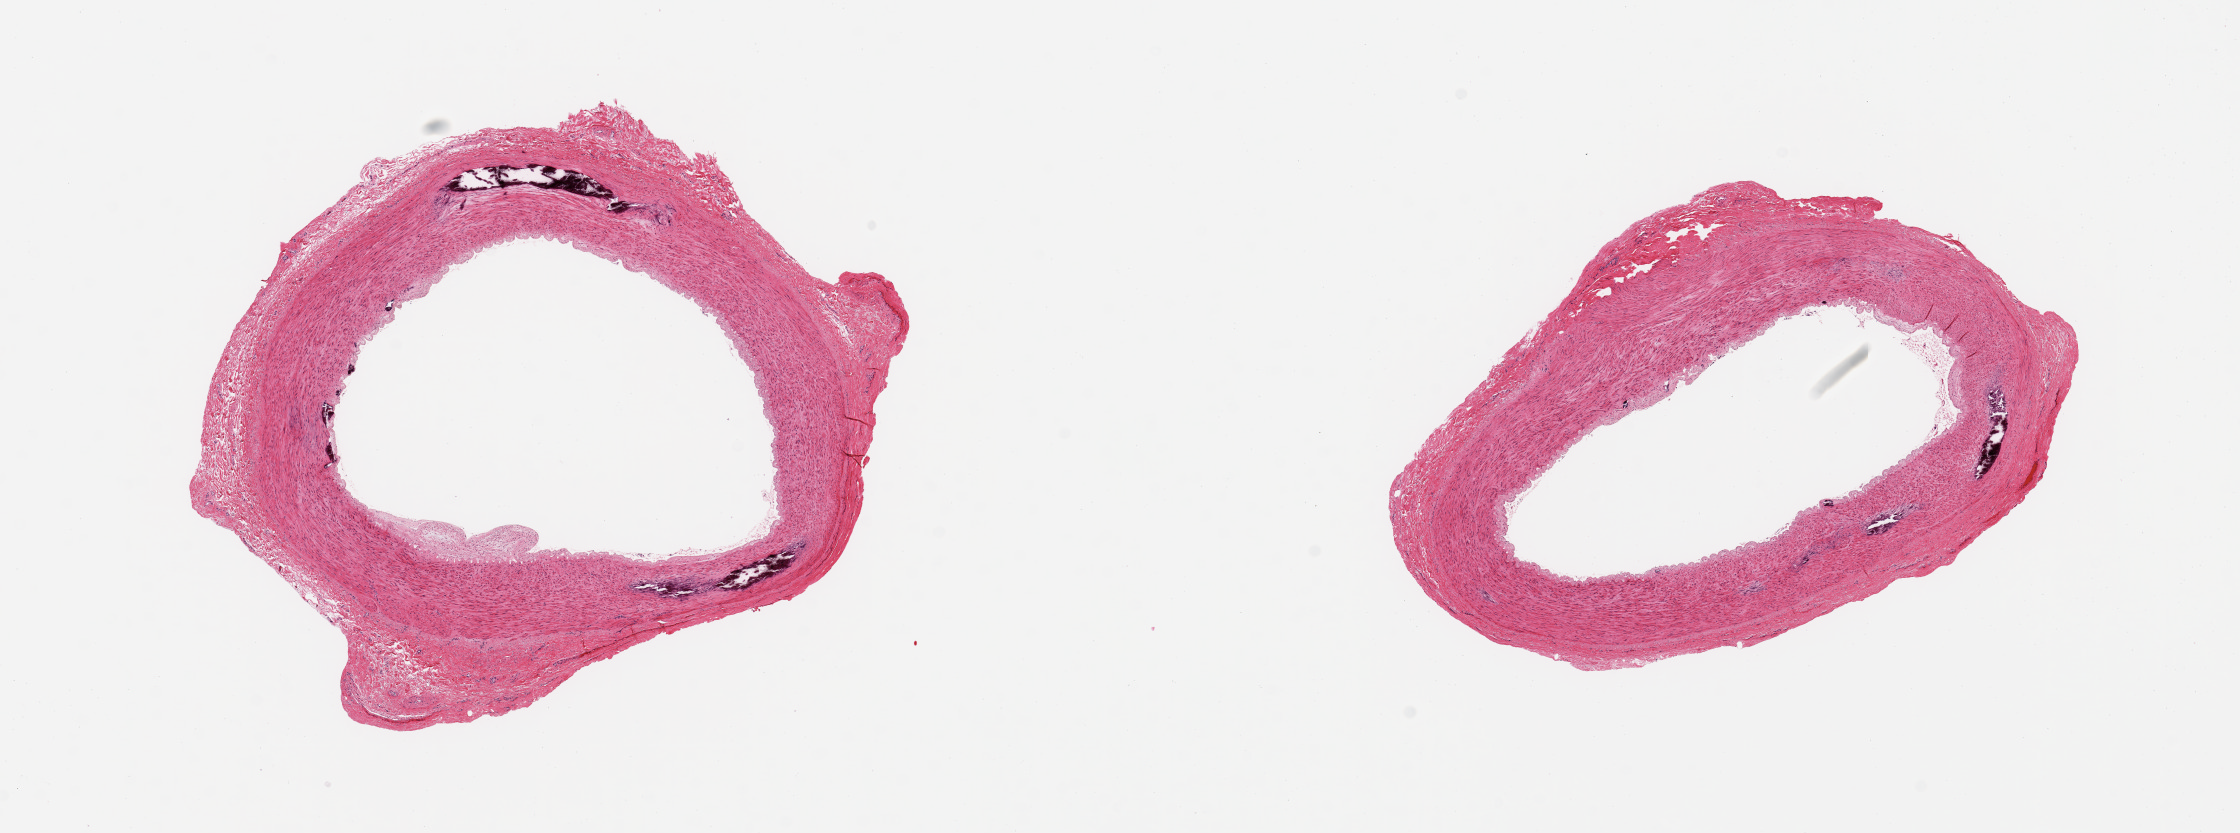
Haematoxylin and eosin whole-slide image, a low-resolution overview of the entire scanned area, about 17.7 x 6.6 mm. PAXgene-fixed paraffin-embedded (PFPE) section. Target tissue: tibial artery. Donor tissue sample. Donor: male.
Pathologist's review note for this sample: 2 pieces; patent lumen, mild plaque and medial calcifications; attached adventitia up to 0.86mm.